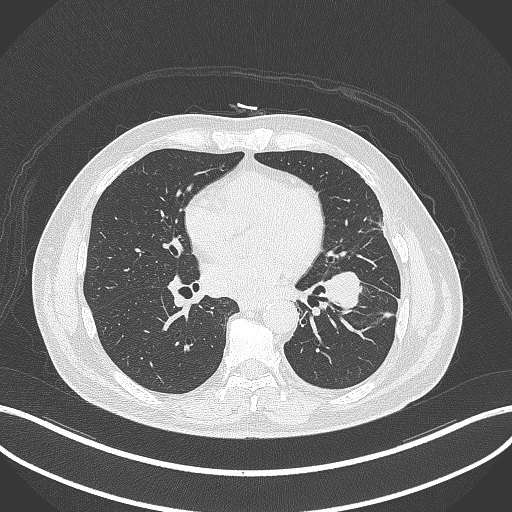
Chest CT, one axial slice. Position 163 of 230 along the scan axis. Reconstruction kernel B70f. Lung window (W 1500 / L -600 HU). 1 mm slice thickness. 512 × 512 image matrix, field of view 400 × 400 mm. Patient: male, 68 years. Case-level facts recorded for this patient, not image findings: clinical TNM (as recorded): T2b N0 M0.
Structures marked on this image (bounding box drawn by a radiologist):
- lung tumour (recorded histology: squamous cell carcinoma): bounding box (x1, y1, x2, y2) in pixels: (322, 267, 367, 314)